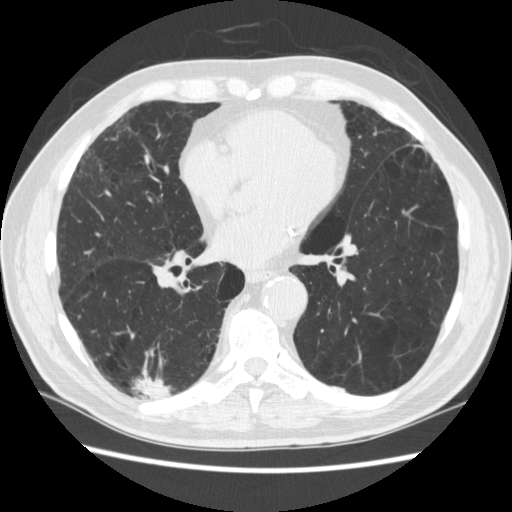
Low-dose screening chest CT, one axial slice; position 119 of 266 along the scan axis; reconstruction kernel STANDARD; lung window (W 1500 / L -600 HU); 1.25 mm slice thickness; 512 × 512 image matrix.
Structures marked on this image (manually delineated by an expert):
- lesion 1 (tumor, upper lobe of right lung): bounding box <134,373,170,399> (left, top, right, bottom; pixels)